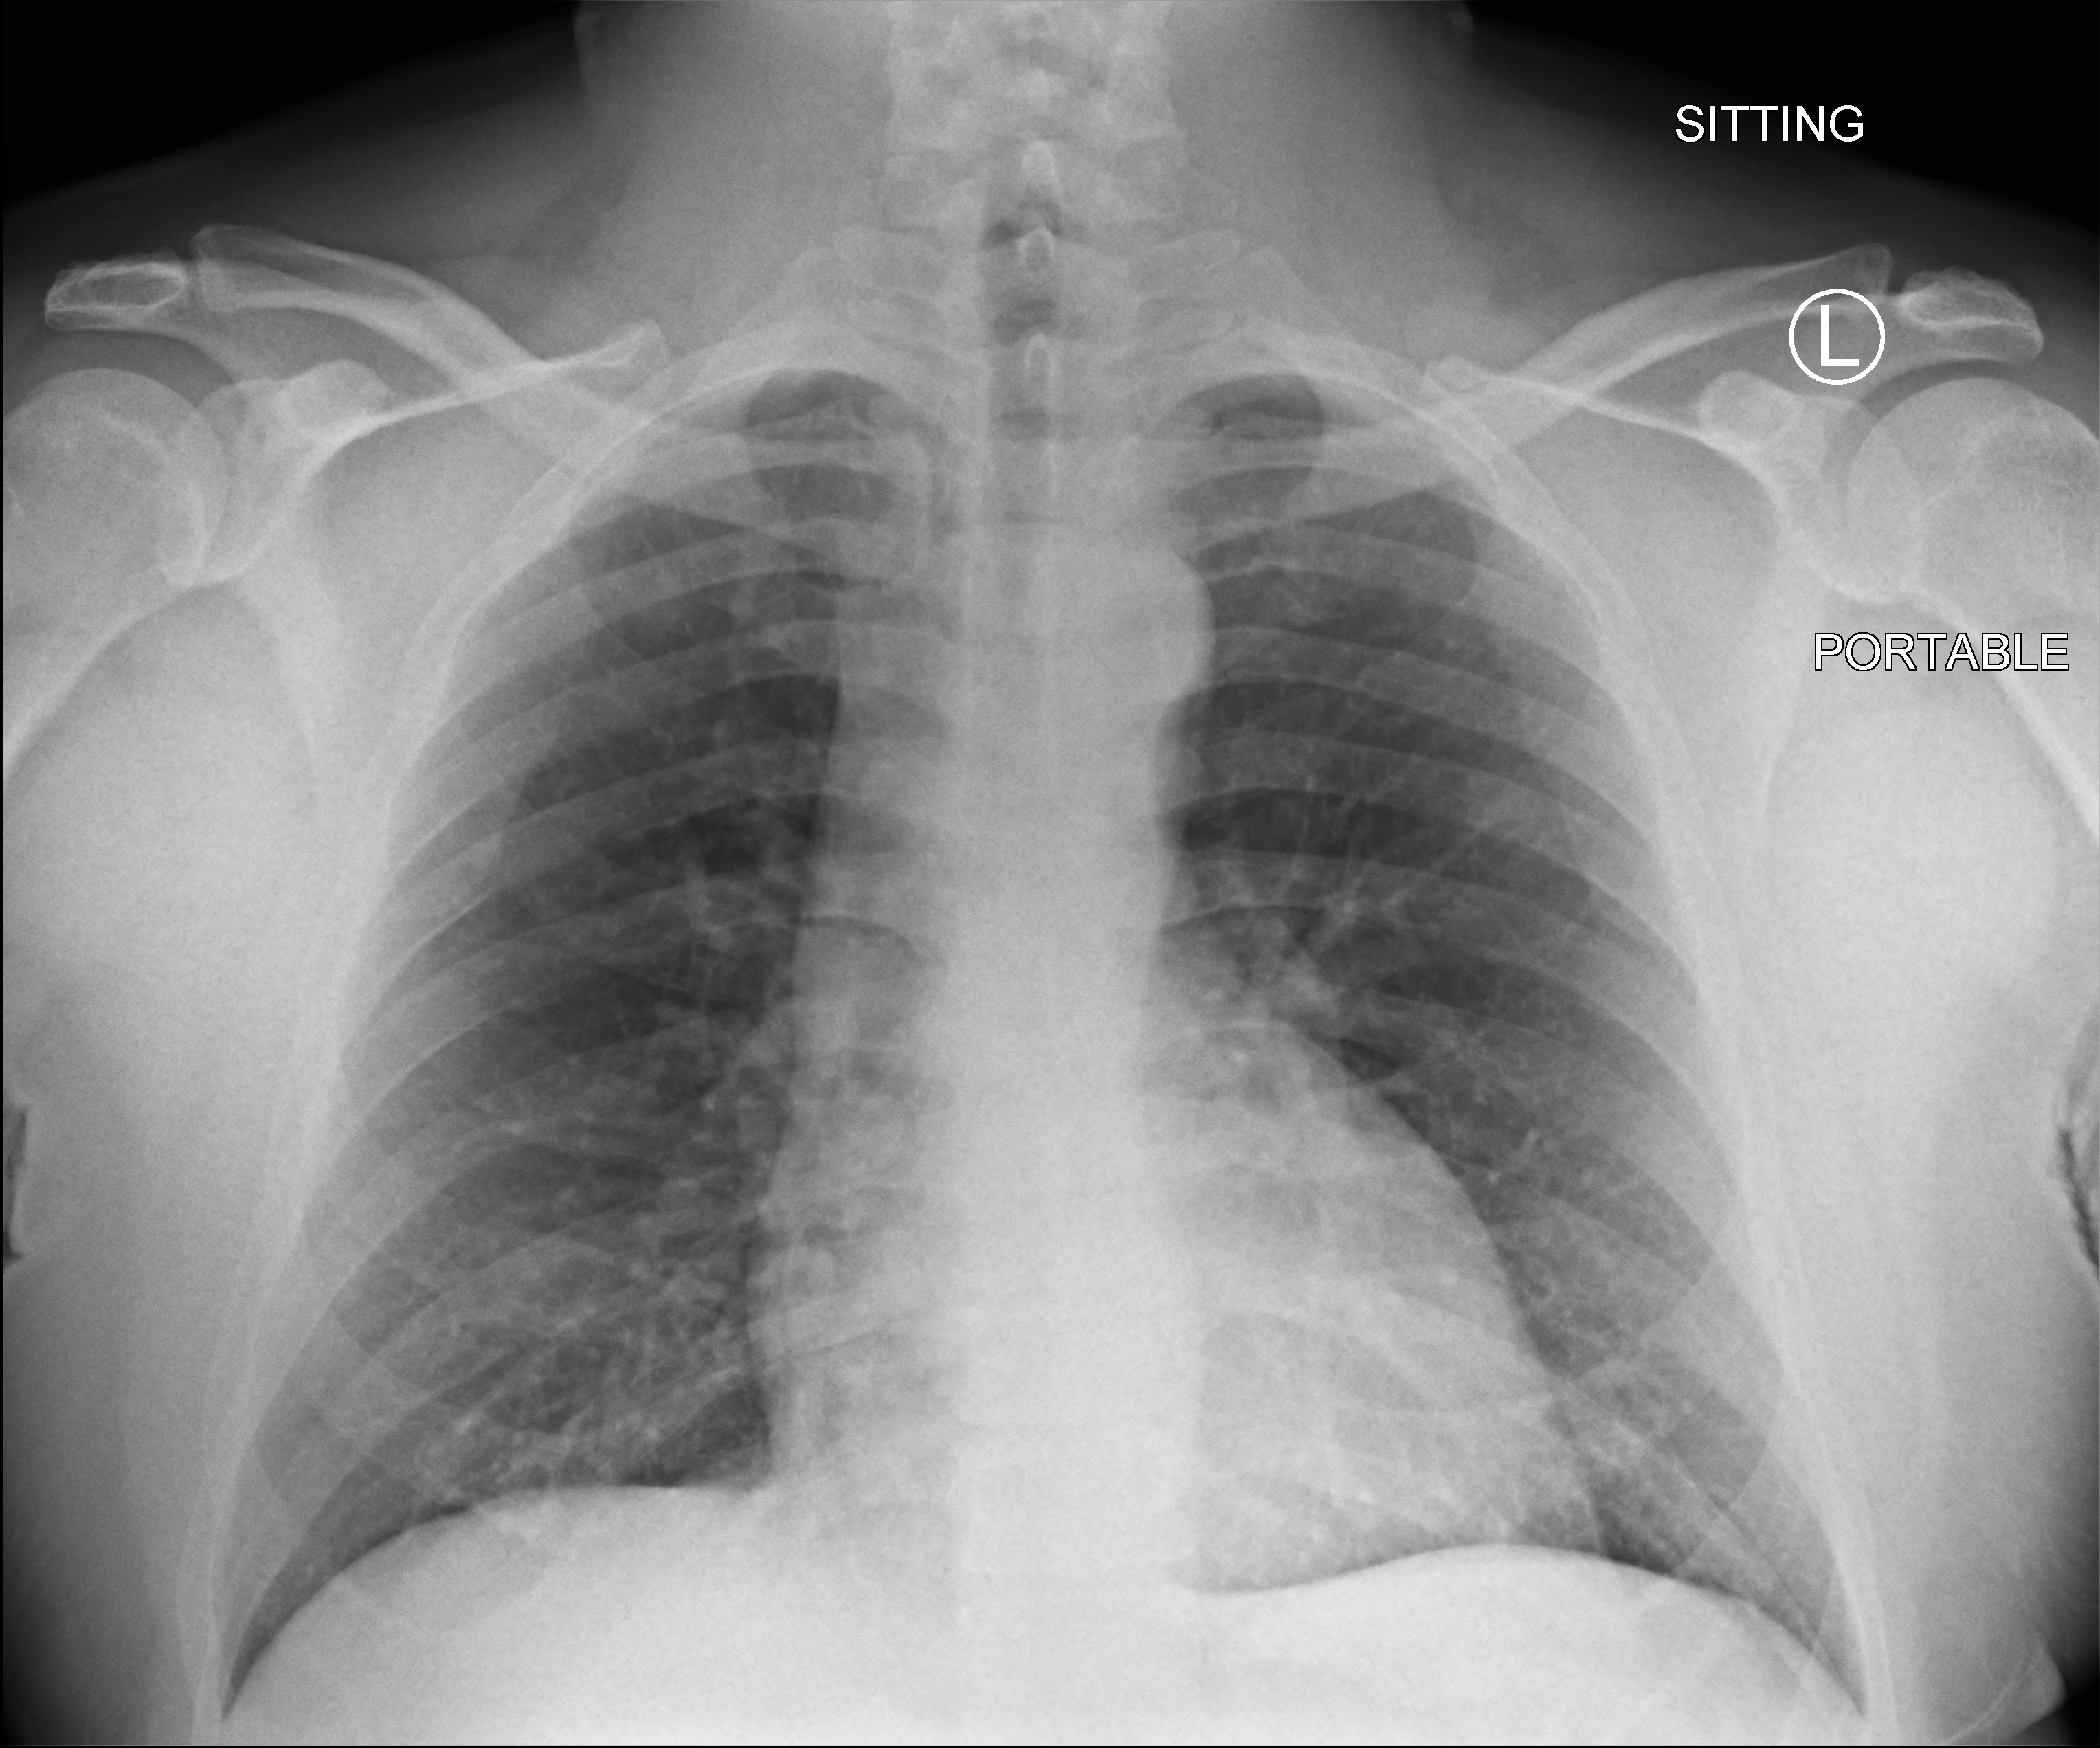
Portable chest radiograph. Male patient hospitalised with COVID-19, age 18–59 years.
From the hospital-stay record, not from the radiograph (when in the stay this image was taken is not recorded):
- admitted to intensive care during this hospital stay: no
- mechanically ventilated during this hospital stay: no